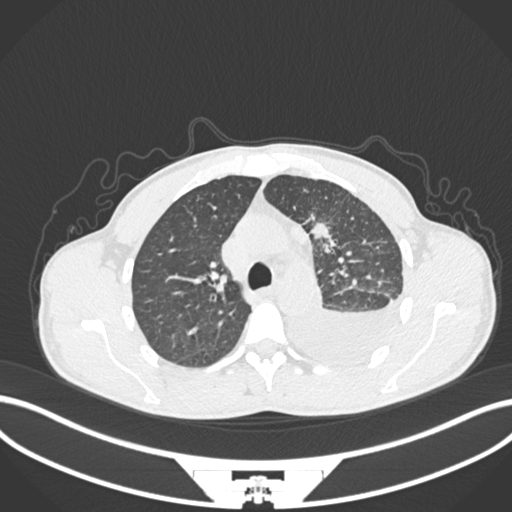
Chest CT, one axial slice. Slice 152 of 244 in the series (ordered by position). 120 kVp. Lung window (W 1500 / L -600 HU). 1 mm slice thickness. 512 × 512 image matrix. Male patient, age 49 years. Case-level facts recorded for this patient, not image findings: clinical TNM (as recorded): T1c N1 M1.
Structures marked on this image (rectangle marked by the reading radiologist):
- lung tumour (recorded histology: adenocarcinoma): box from (x=311, y=212) to (x=340, y=254) px